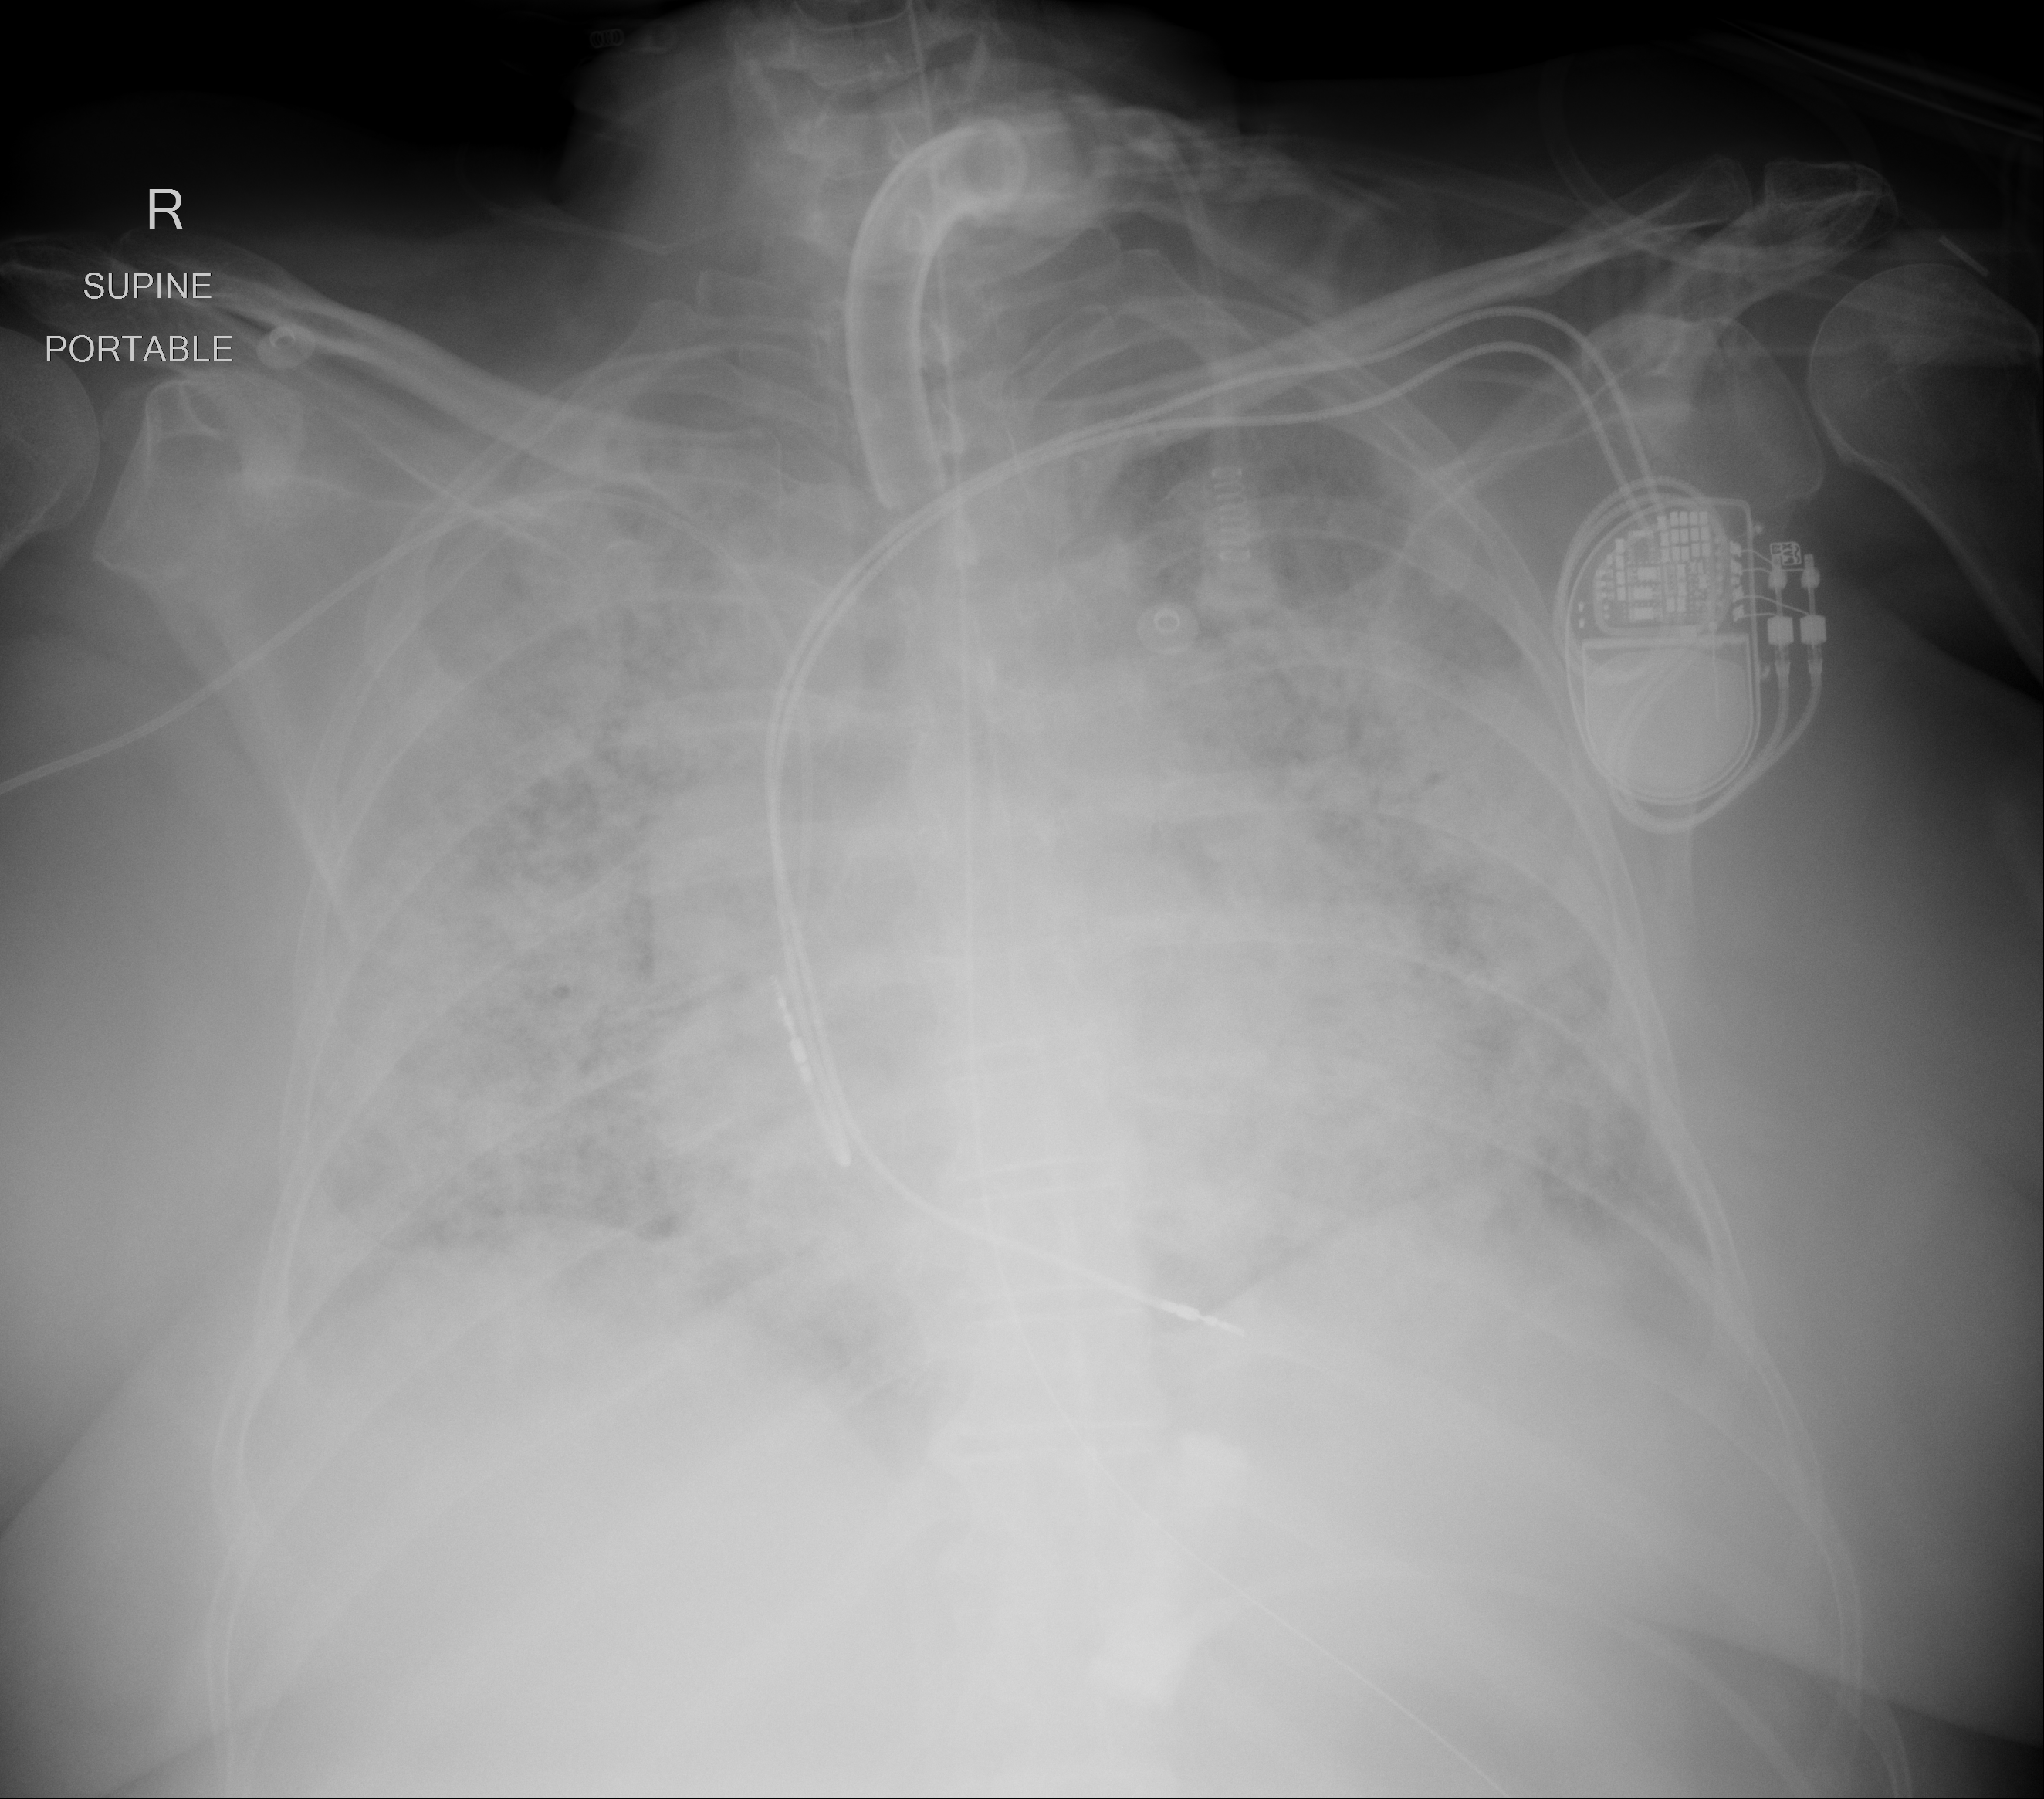
Portable chest radiograph, AP projection. Female patient, age 57 years; imaged 30 days after the COVID-19 diagnosis.
Key findings recorded by the radiologist: Diffuse multifocal consolidation involving both lungs is seen and is worsened.